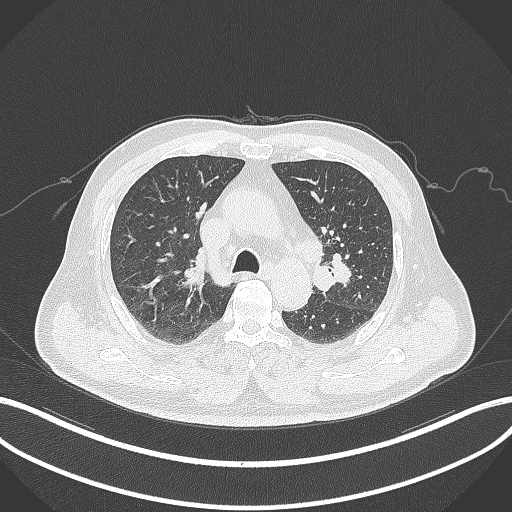
Chest CT, one axial slice; position 203 of 286 along the scan axis; reconstruction kernel B70f; lung window (W 1500 / L -600 HU); 1 mm slice thickness; 512 × 512 image matrix. Patient: male, 67 years. From the clinical record (not read from this slice): clinical TNM (as recorded): T2a N1 M0; histopathological grade: G3.
Structures marked on this image (rectangle marked by the reading radiologist):
- lung tumour (recorded histology: adenocarcinoma): bounding box <310,253,358,295> (left, top, right, bottom; pixels)